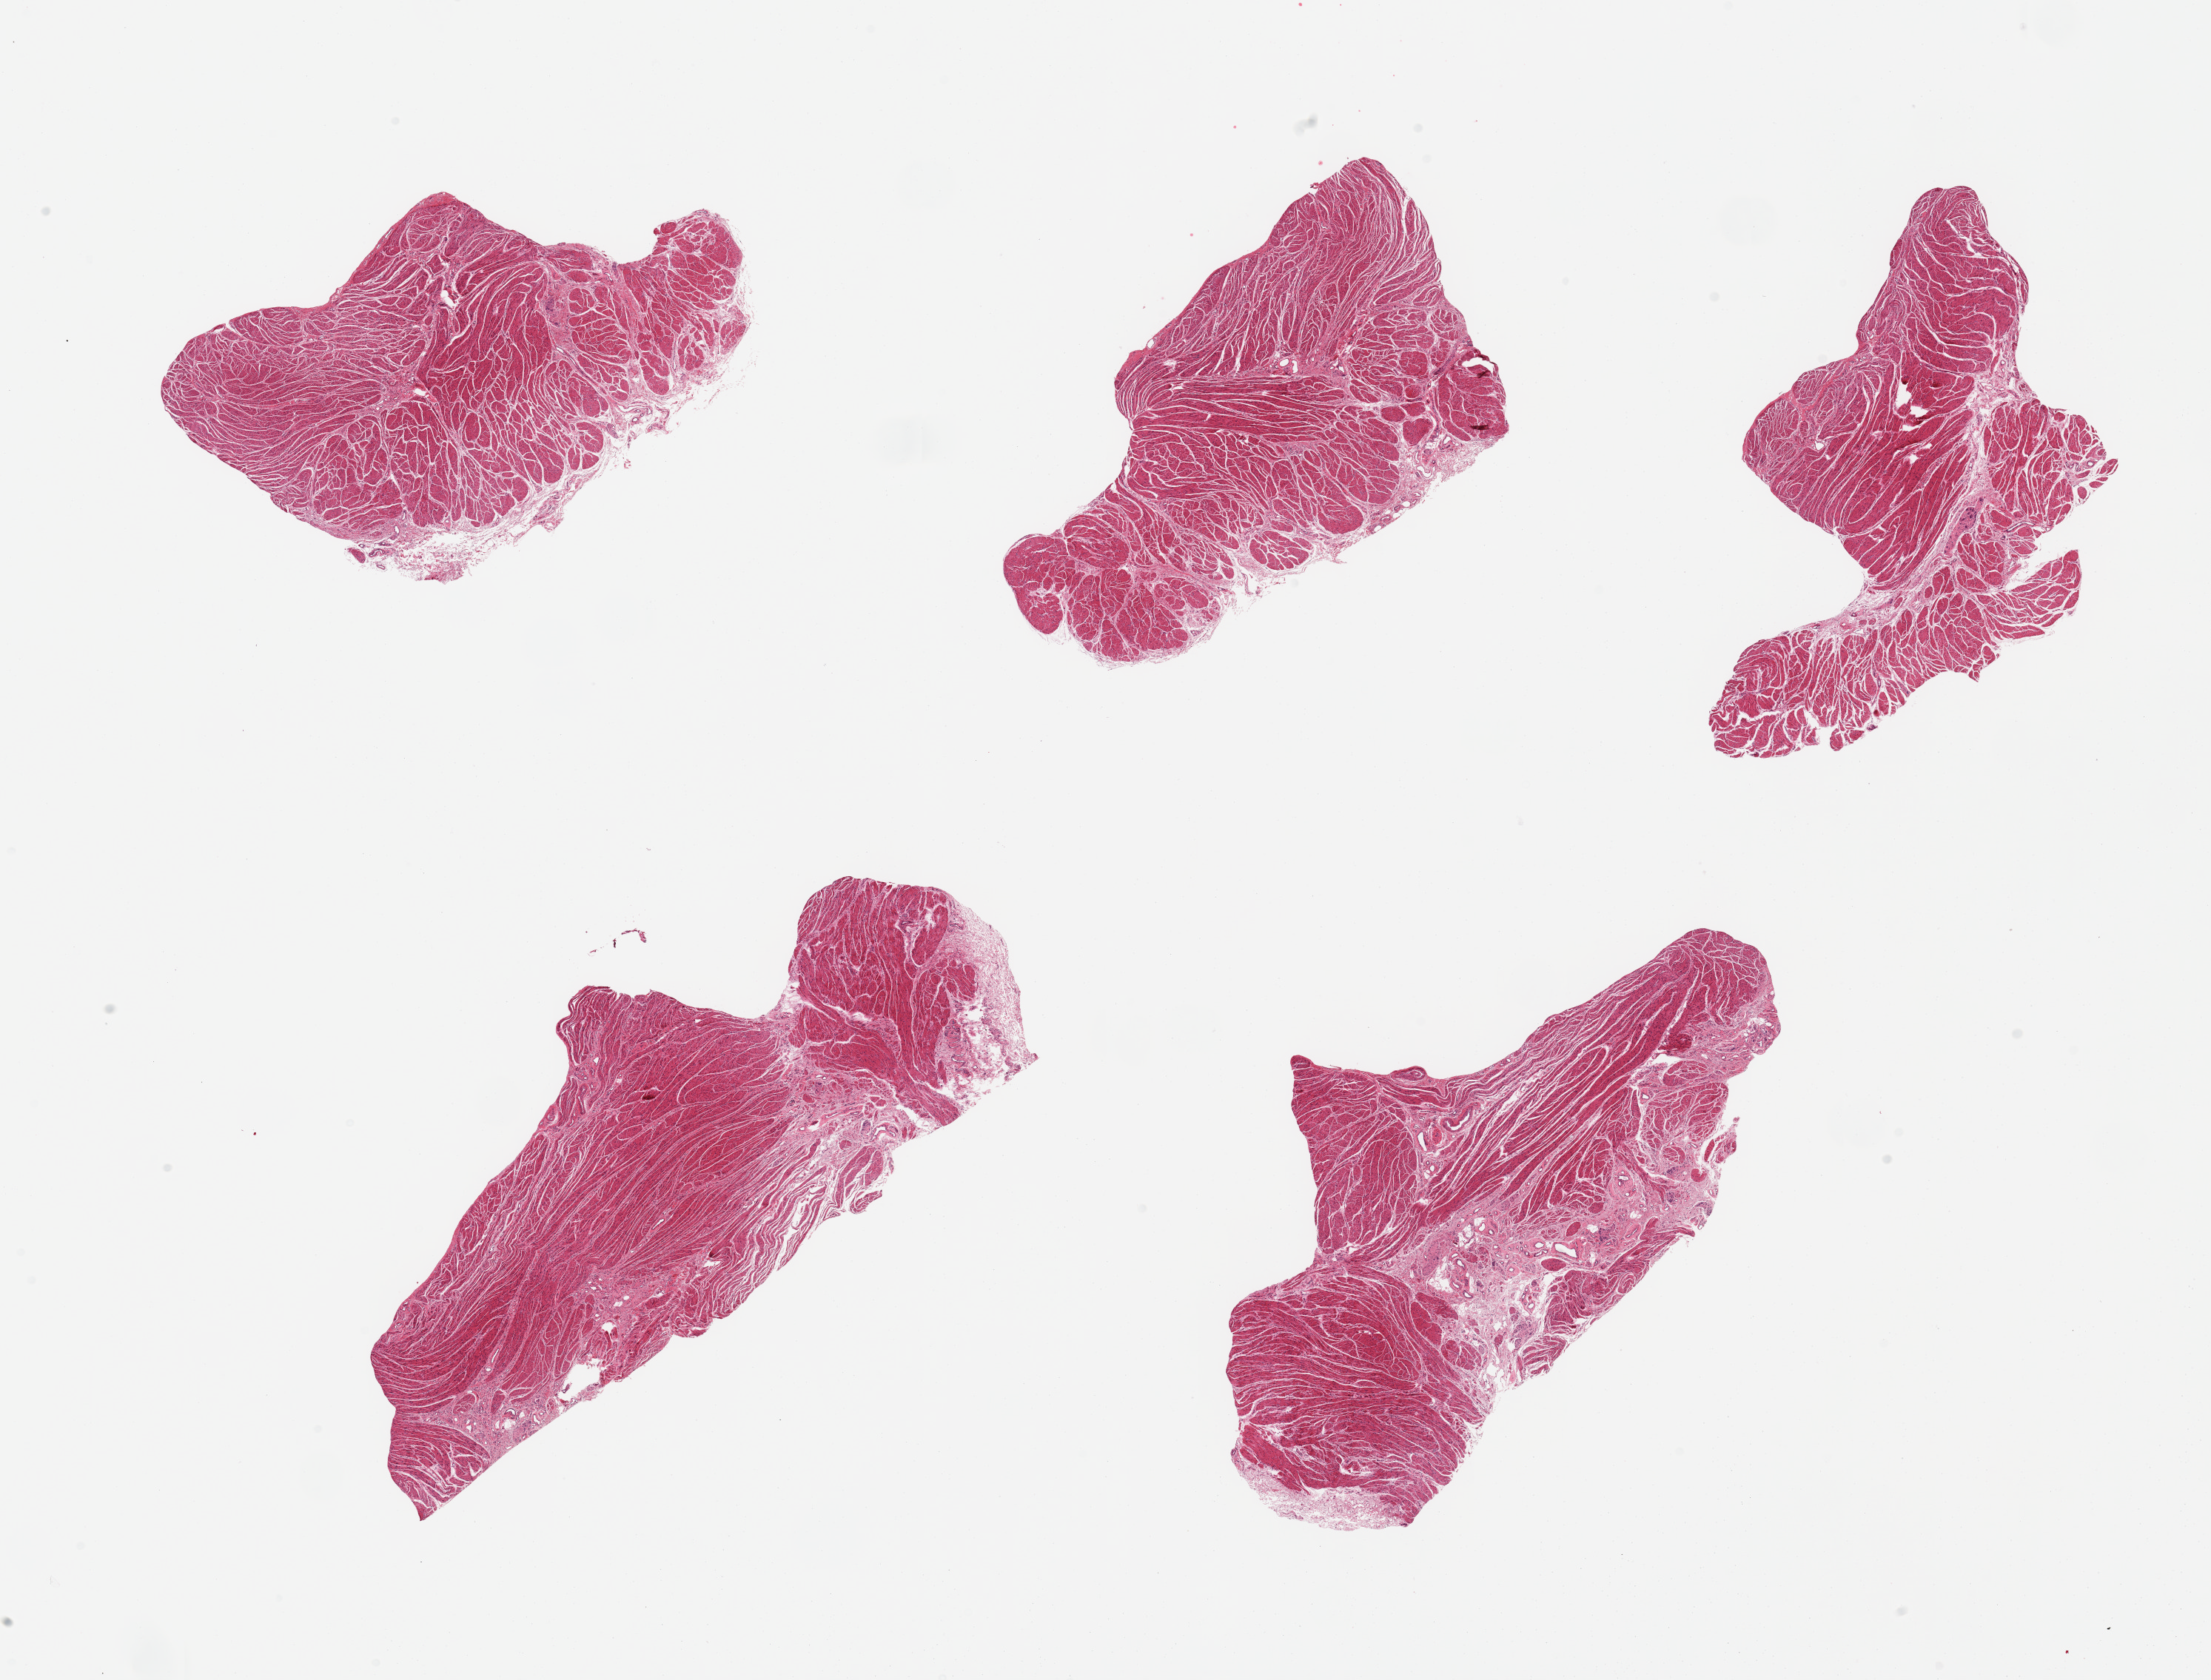
Hematoxylin and eosin (H&E) whole-slide image, whole scanned area (about 23.6 x 18.0 mm, from a 20x scan) shown as a low-resolution overview, PAXgene-fixed, paraffin-embedded tissue, sampled site (target tissue): gastroesophageal junction, donor tissue sample. Donor: female.
Review note (as recorded): 5 pieces; well trimmed.